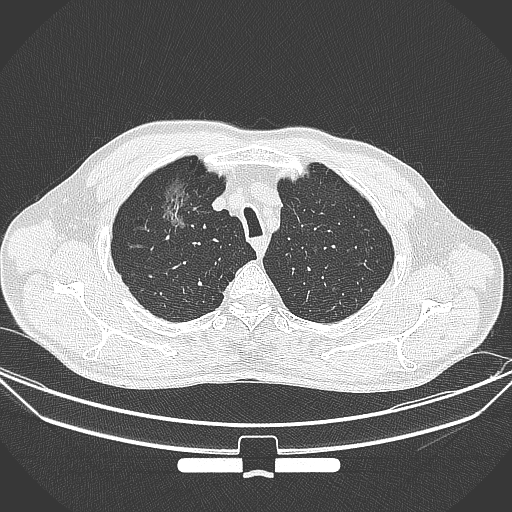
Chest CT, one axial slice; slice 288 of 355 in the series (ordered by position); lung window (W 1500 / L -600 HU); 1 mm slice thickness; 512 × 512 image matrix, field of view 399 × 399 mm. Male patient, age 67 years. From the clinical record (not read from this slice): clinical TNM (as recorded): T1c N0 M0.
Outlined on this slice (rectangle marked by the reading radiologist):
- lung tumour (recorded histology: adenocarcinoma): bounding box <152,176,194,242> (left, top, right, bottom; pixels)